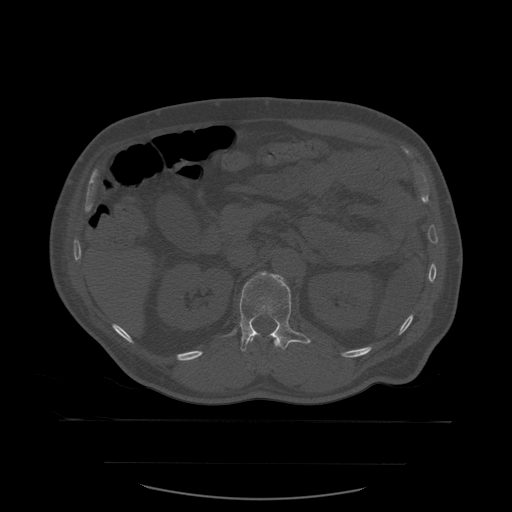
CT including the spine, one axial slice; position 250 of 590 along the scan axis; bone window (W 1800 / L 400 HU); 512 × 512 image matrix, field of view 479 × 479 mm. Patient age 71 years. From the clinical record (not read from this slice): primary cancer: lung; vertebrae with lytic lesions (as recorded): T1, T2, L5, S1.
Annotated regions visible in this slice (semi-automatically segmented with operator editing):
- L1 vertebra: bounding box <224,272,311,352> (left, top, right, bottom; pixels)
- T12 vertebra: <274,340,286,351>